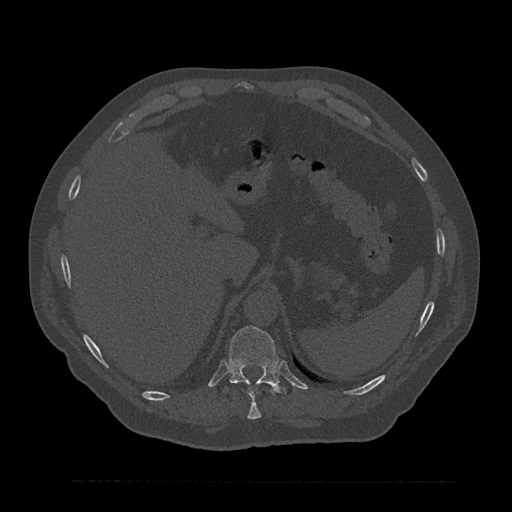
CT including the spine, one axial slice; slice 314 of 797 in the series (ordered by position); bone window (W 1800 / L 400 HU); 0.5 mm slice thickness; 512 × 512 image matrix. Male patient, age 61 years. From the clinical record (not read from this slice): primary cancer: prostate.
Outlined on this slice (semi-automatically segmented with operator editing):
- T10 vertebra: box from (x=247, y=390) to (x=262, y=420) px
- T11 vertebra: (x=229, y=326)–(x=287, y=394)